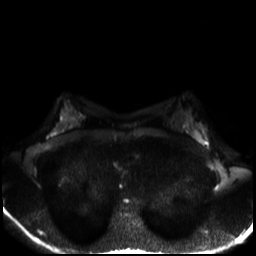
Breast MRI, one axial slice. Position 18 of 30 along the scan axis. Diffusion-weighted series; image 2 of 4 stored at this slice position (different b-values; order by instance number). 3 T. 4 mm slice thickness. 256 × 256 image matrix, field of view 320 × 320 mm. Female patient.
Annotated regions visible in this slice (manually delineated by an expert):
- tumour on diffusion-weighted imaging: bounding box (x1, y1, x2, y2) in pixels: (194, 131, 201, 142)